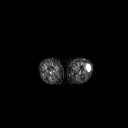
FDG PET of an extremity soft-tissue mass (from a PET/CT study), one axial slice. Position 179 of 223 along the scan axis. 128 × 128 image matrix, field of view 700 × 700 mm. Female patient, age 16 years. Case-level facts recorded for this patient, not image findings: histological type: spindle cell suggestive of biphasic synovial sarcoma; grade: intermediate; site of the primary tumour: left knee.
Annotated regions visible in this slice (expert contour drawn on MRI and transferred to this co-registered scan by the dataset authors):
- gross tumour volume including surrounding oedema: bounding box <86,62,91,71> (left, top, right, bottom; pixels)
- gross tumour volume (mass): <86,62,91,71>